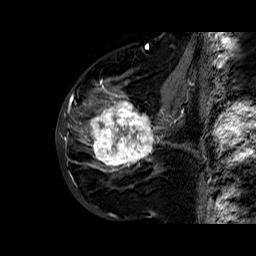
Breast MRI (dynamic contrast-enhanced), one sagittal slice. Slice 25 of 60 in the series (ordered by position). Dynamic contrast-enhanced series, time point 2 of 6 at this slice position (early post-contrast). 1.5 T. TE 6.4 ms, TR 32.8 ms. 4 mm slice thickness. 256 × 256 image matrix. Female patient. Case-level facts recorded for this patient, not image findings: setting: breast cancer imaged before/during neoadjuvant chemotherapy; receptor status: HR-positive, HER2-negative.
Outlined on this slice (semi-automatically segmented with operator editing):
- analysis volume of interest (the breast-tissue region the enhancement analysis was run in; not a lesion): box from (x=86, y=77) to (x=163, y=177) px
- tumour enhancement mask (voxels above the 100 % enhancement threshold inside the analysis volume of interest): (x=89, y=79)–(x=159, y=171)